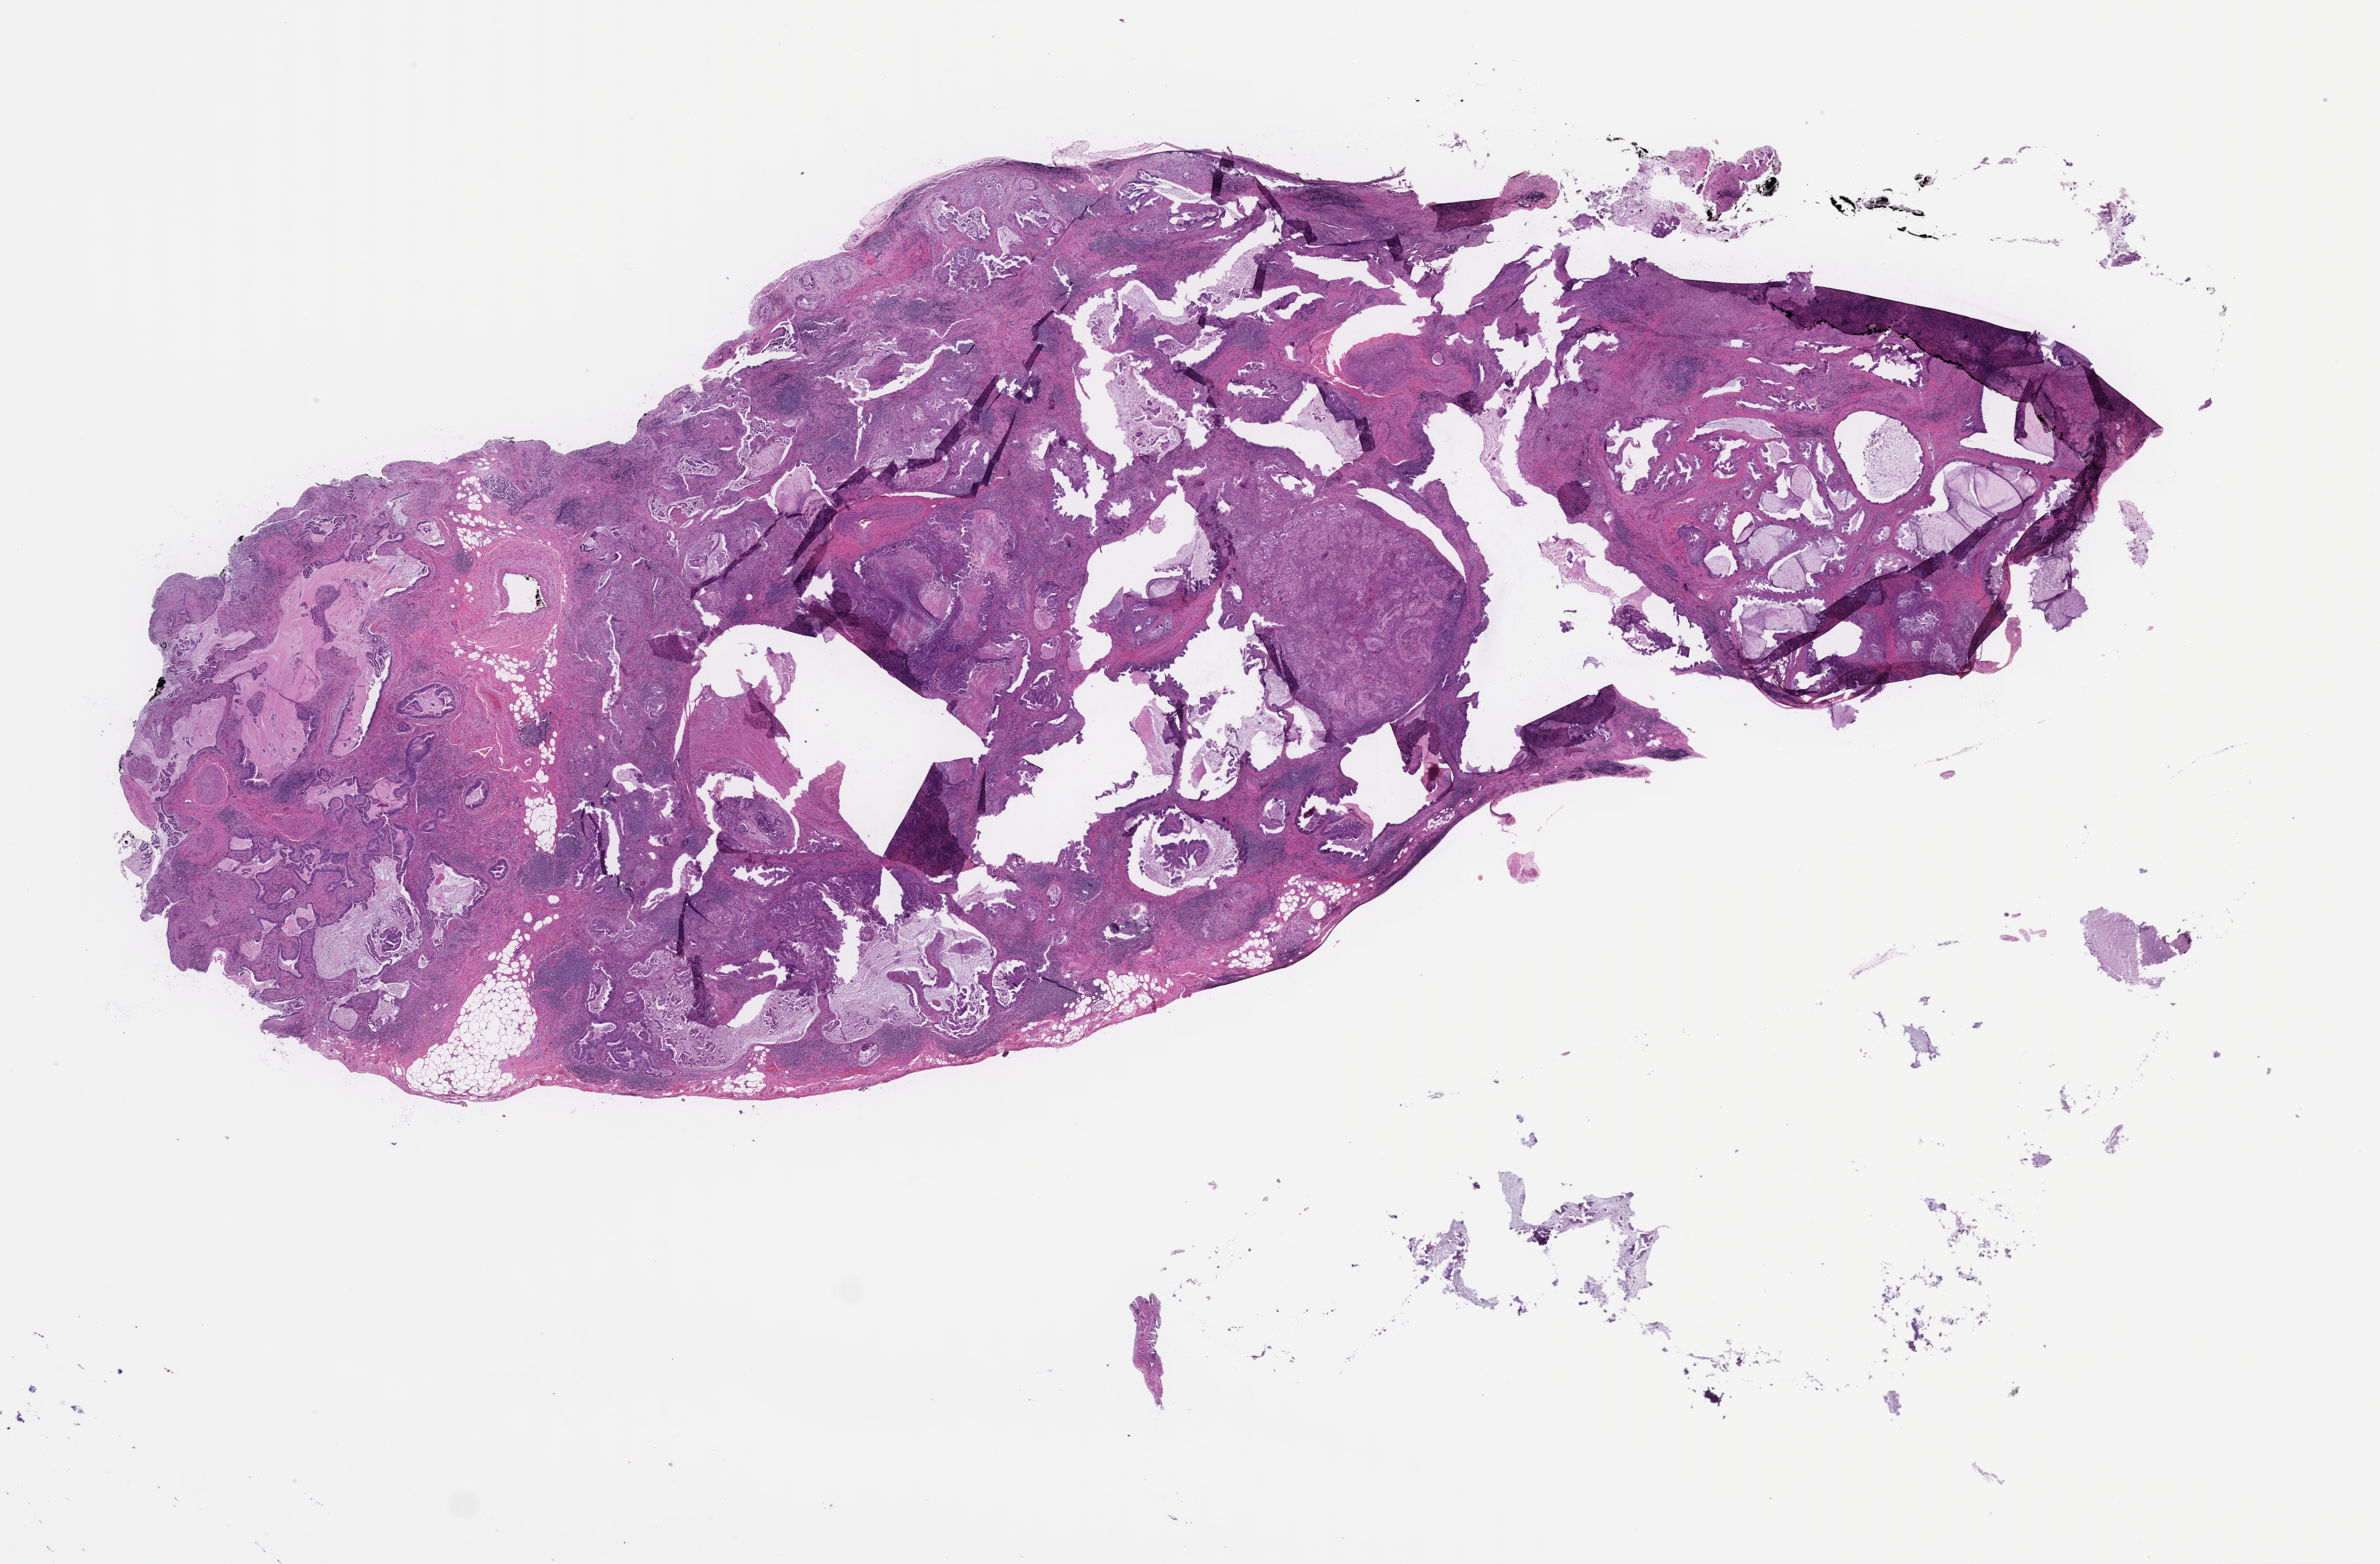
Haematoxylin and eosin whole-slide image — shown as a low-resolution overview of the whole scanned area (about 28.6 x 18.8 mm). FFPE section. Tissue site: lung. Specimen time point: archival tissue. Patient sex: male.
• this section: primary tumour tissue
• diagnosis: Non-Small Cell Lung Carcinoma